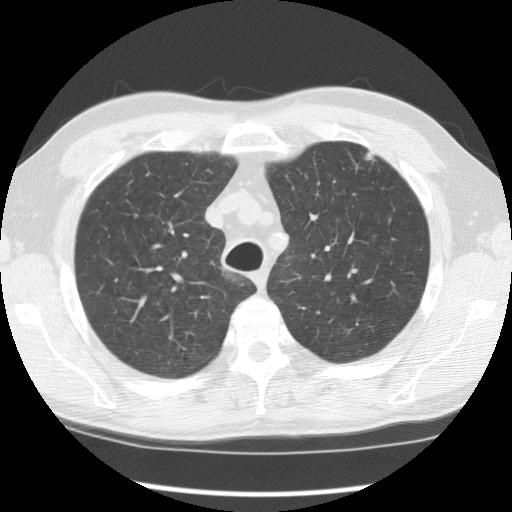
Low-dose screening chest CT, one axial slice. Position 94 of 121 along the scan axis. Reconstruction kernel STANDARD. Lung window (W 1500 / L -600 HU). 2.5 mm slice thickness. 512 × 512 image matrix, field of view 350 × 350 mm.
Structures marked on this image (outlined manually by an expert reader):
- lesion 1 (tumor, upper lobe of left lung): bounding box (x1, y1, x2, y2) in pixels: (365, 152, 374, 160)